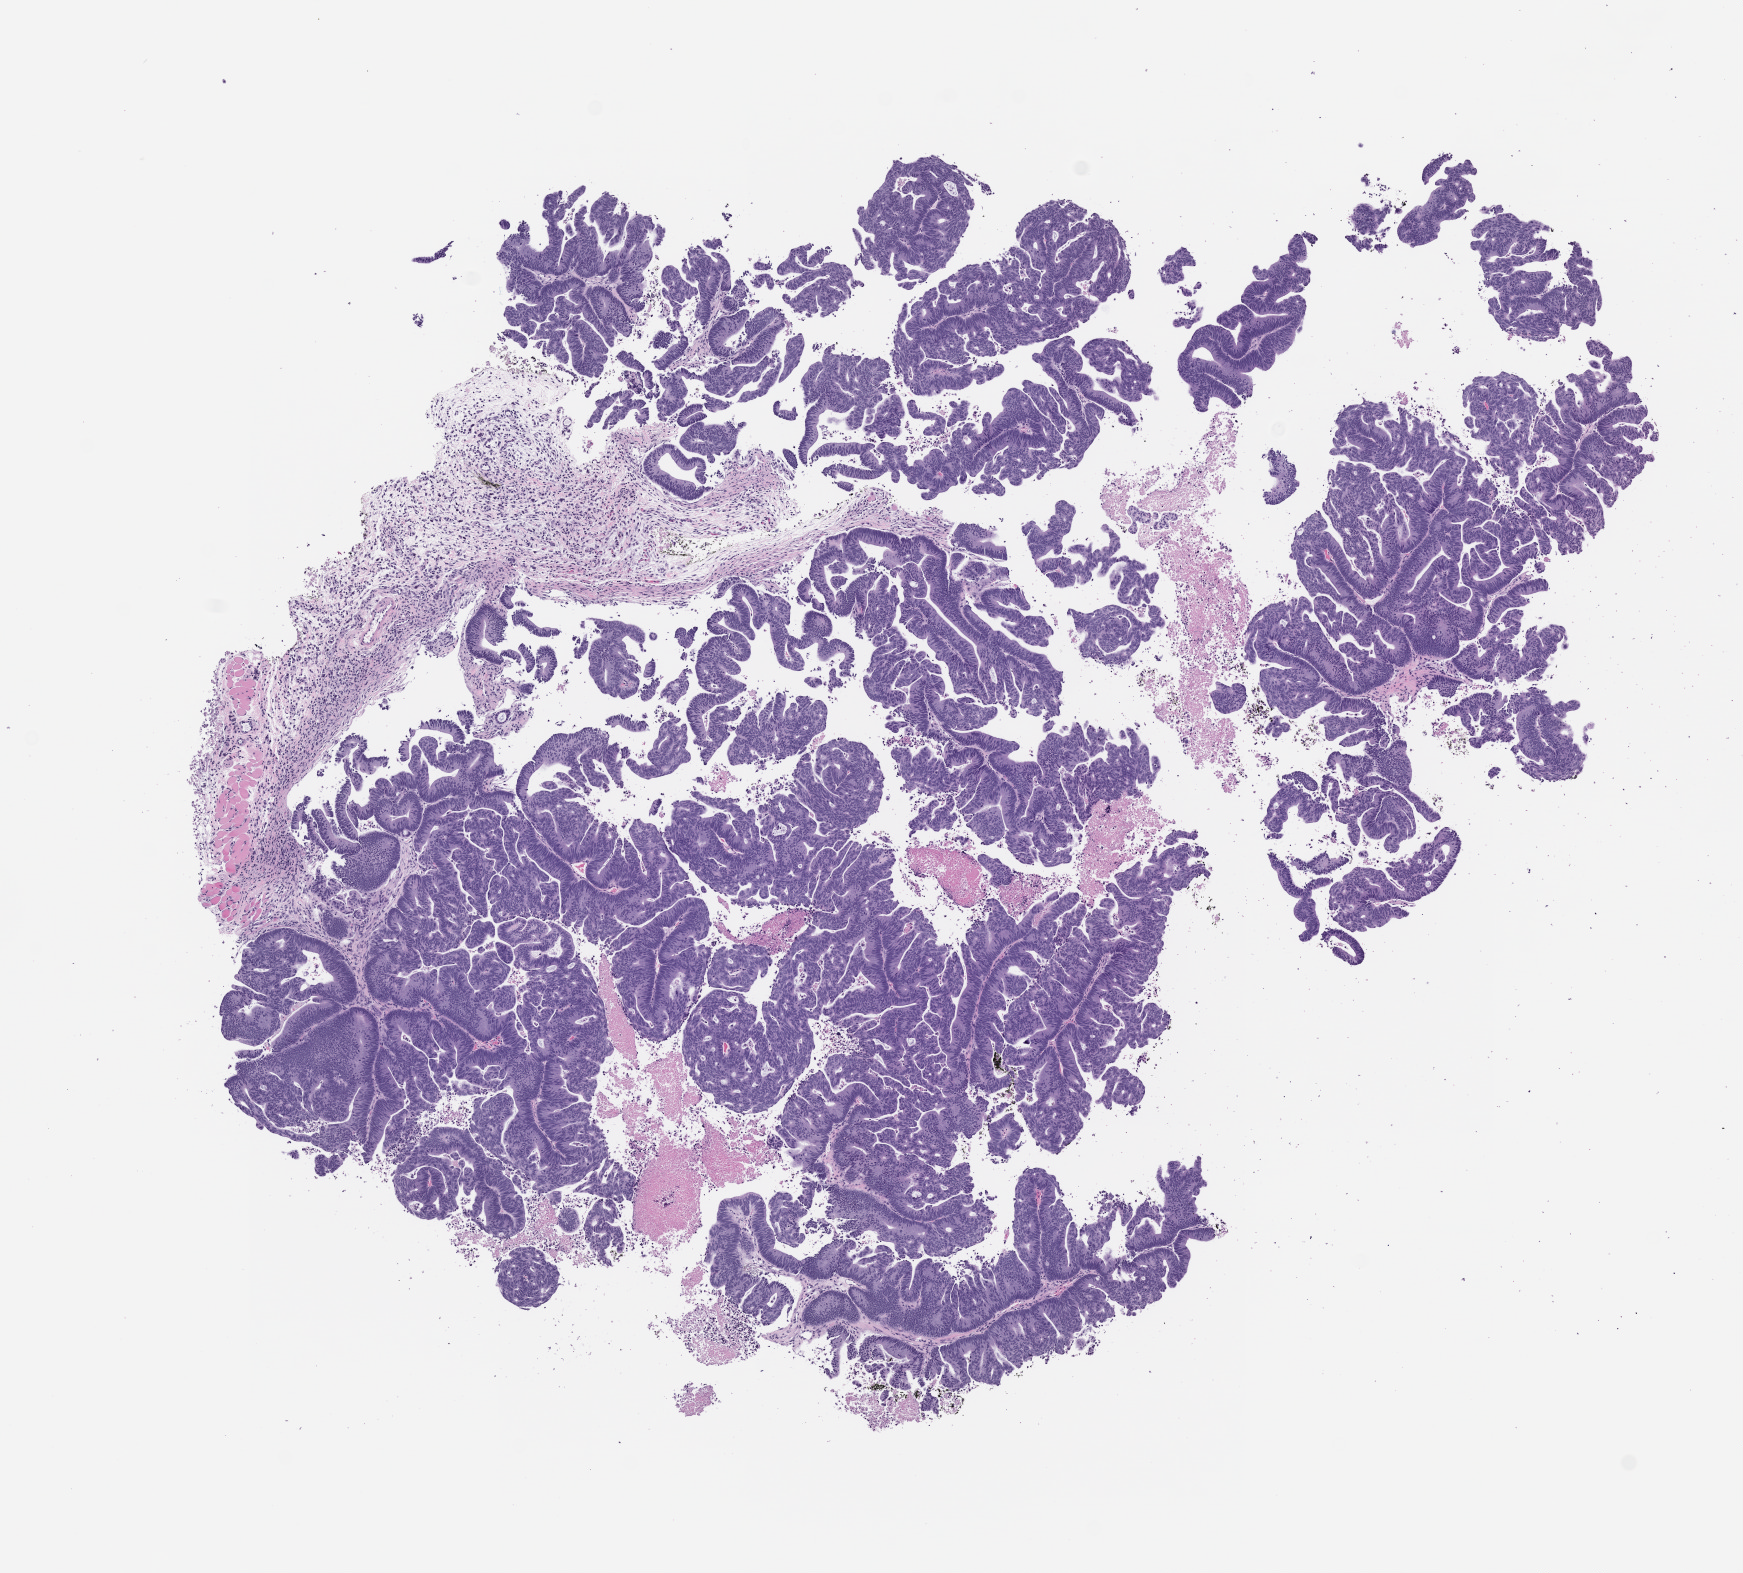
Whole-slide image, hematoxylin and eosin (H&E): patient-derived xenograft (human tumor grown in a mouse), passage 2, low-resolution overview of the scanned area, about 7.0 x 6.3 mm; formalin-fixed paraffin-embedded section; originating tumor site category: gastrointestinal tract.
* originating patient diagnosis: Colorectal Carcinoma